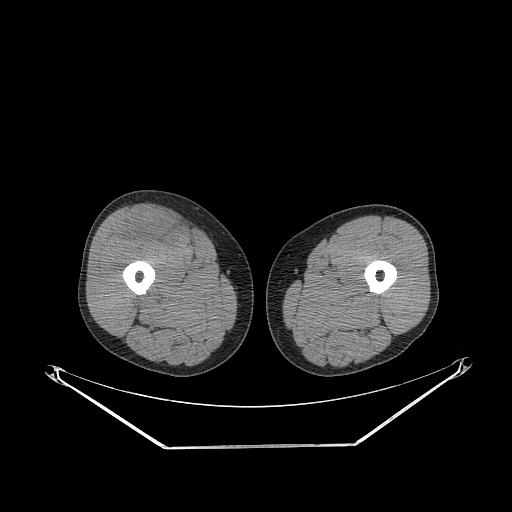
CT of an extremity soft-tissue mass (from a PET/CT study), one axial slice. Slice 263 of 311 in the series (ordered by position). Soft-tissue window (W 400 / L 40 HU). 512 × 512 image matrix, field of view 500 × 500 mm. Male patient. From the clinical record (not read from this slice): histological type: pleiomorphic leiomyosarcoma; grade: intermediate; site of the primary tumour: right thigh.
Structures marked on this image (expert contour drawn on MRI and transferred to this co-registered scan by the dataset authors):
- gross tumour volume including surrounding oedema: bounding box (x1, y1, x2, y2) in pixels: (128, 208, 179, 243)
- gross tumour volume (mass): (142, 217, 163, 238)